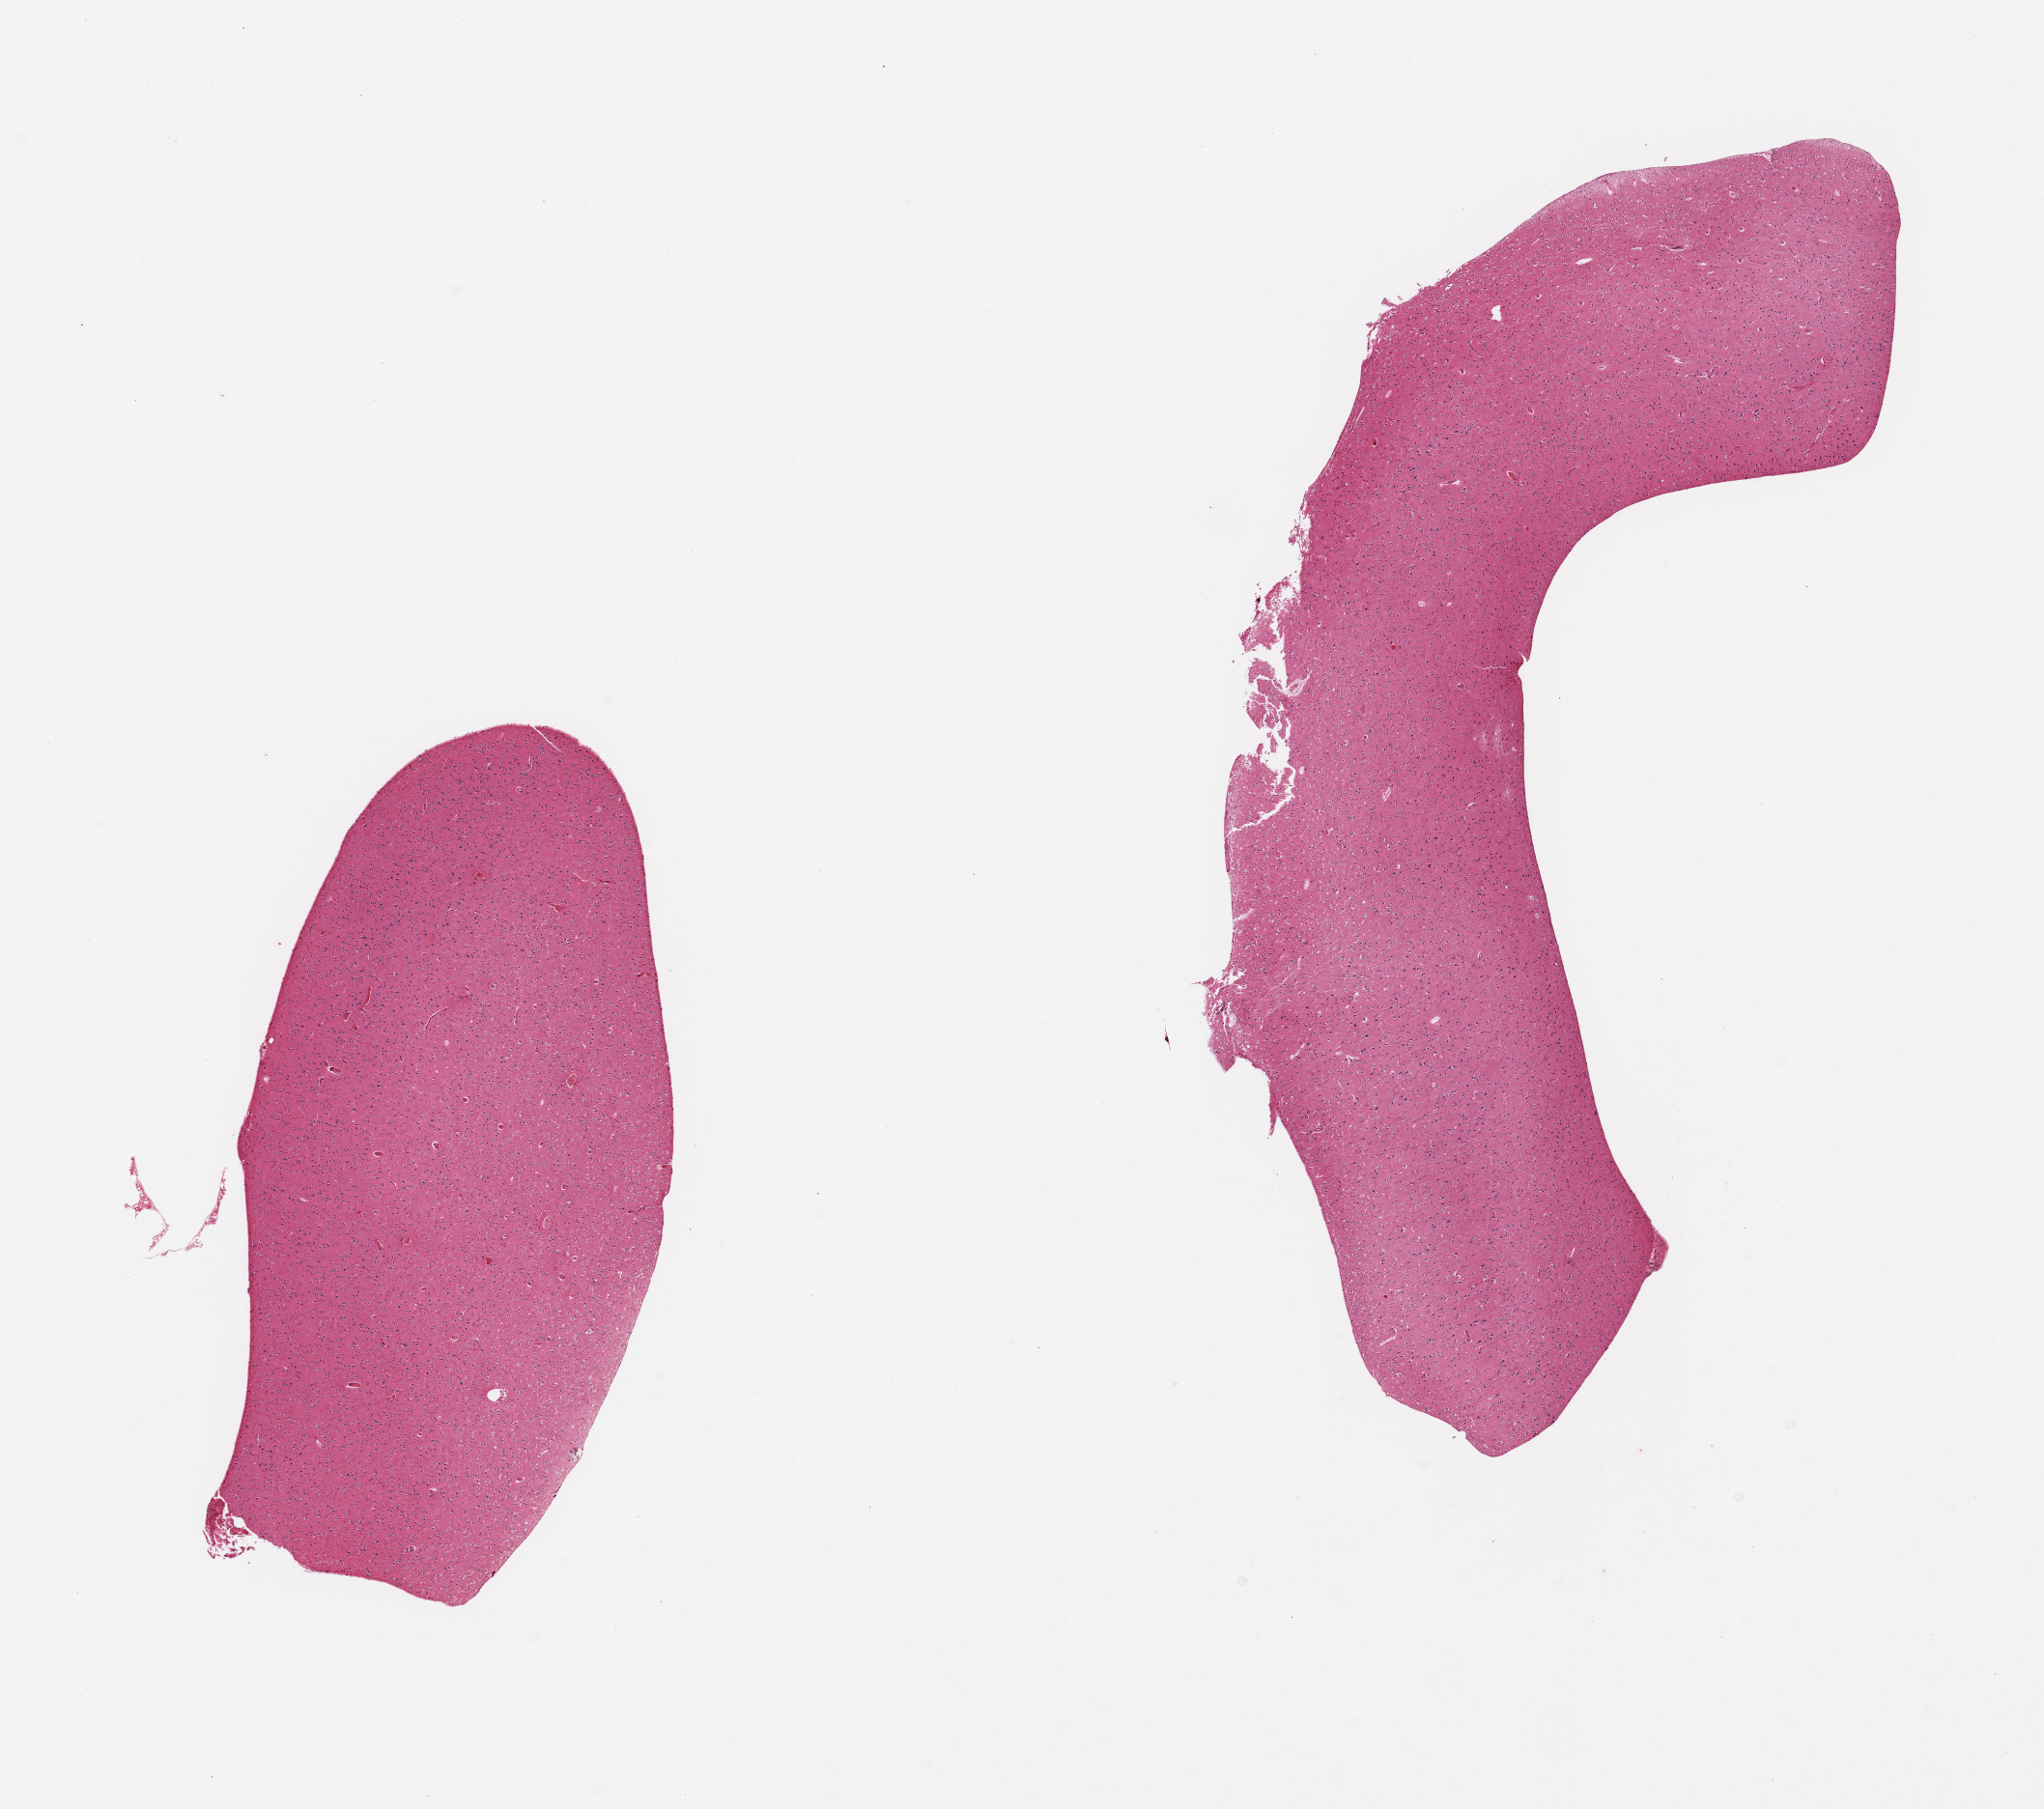
Digitized hematoxylin and eosin (H&E)-stained section — low-resolution overview of the scanned area, about 16.7 x 14.8 mm (slide scanned at 20x), PAXgene-fixed paraffin-embedded (PFPE) section, section of cerebral cortex (target tissue), tissue donor sample.
Review note (as recorded): 2 pieces.